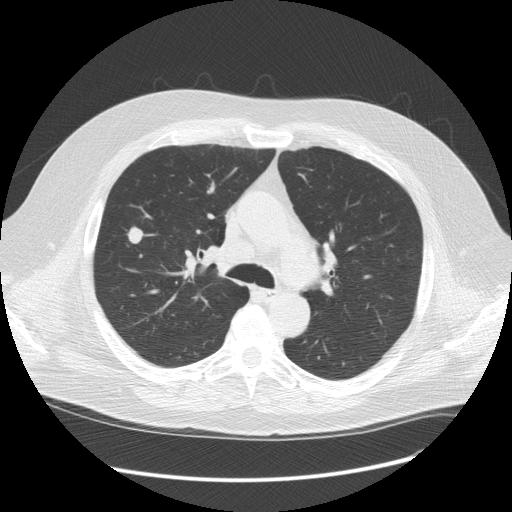
Low-dose screening chest CT, one axial slice. Position 86 of 128 along the scan axis. Reconstruction kernel STANDARD. Lung window (W 1500 / L -600 HU). 2.5 mm slice thickness. 512 × 512 image matrix, field of view 401 × 401 mm.
Outlined on this slice (manually delineated by an expert):
- lesion 1 (tumor, upper lobe of right lung): bounding box <128,227,143,244> (left, top, right, bottom; pixels)